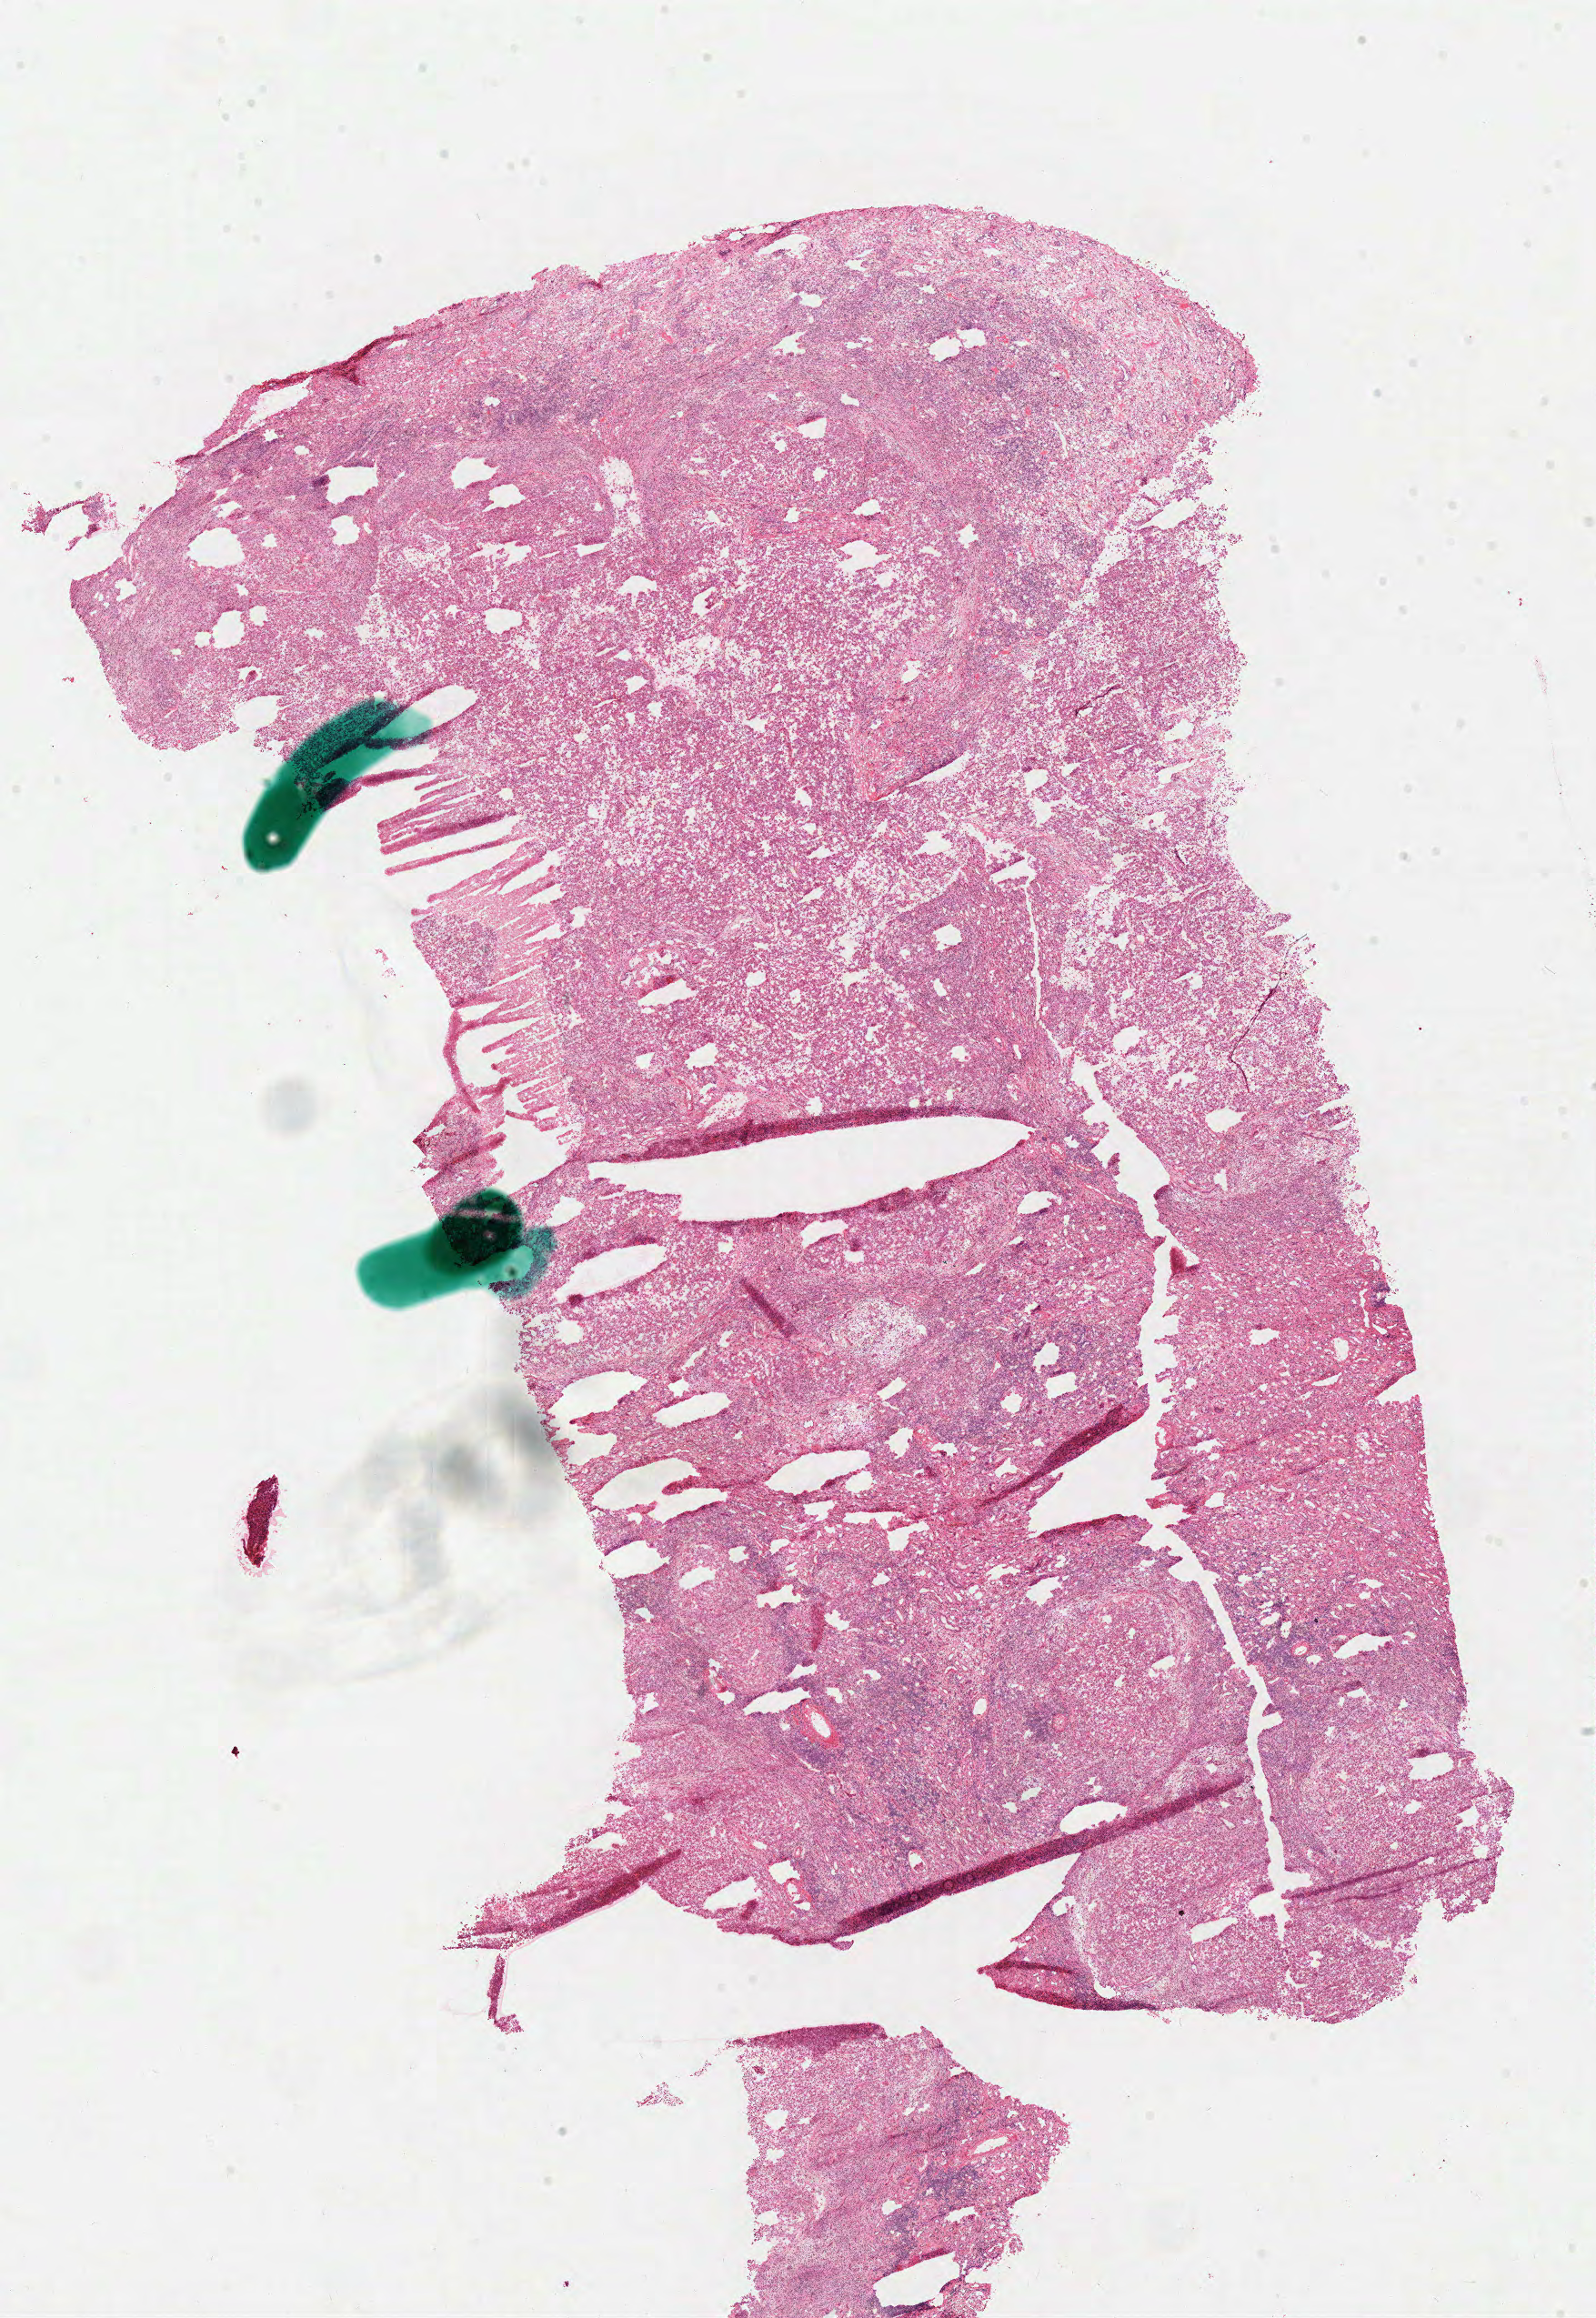
Digitized H&E tissue section (whole slide) — whole scanned area (about 13.8 x 20.1 mm) shown as a low-resolution overview, frozen section, primary tumour sample from the kidney. Male, age 63 years at initial diagnosis. Pathologist review of this section (percent, as recorded): tumour cells 65%, tumour nuclei 65%, normal cells 20%, stromal cells 10%, necrosis 5%.
• AJCC pathologic stage: IV
• lymph nodes positive (case pathology): 21 of 32 examined
• pathologic diagnosis: Papillary adenocarcinoma, NOS